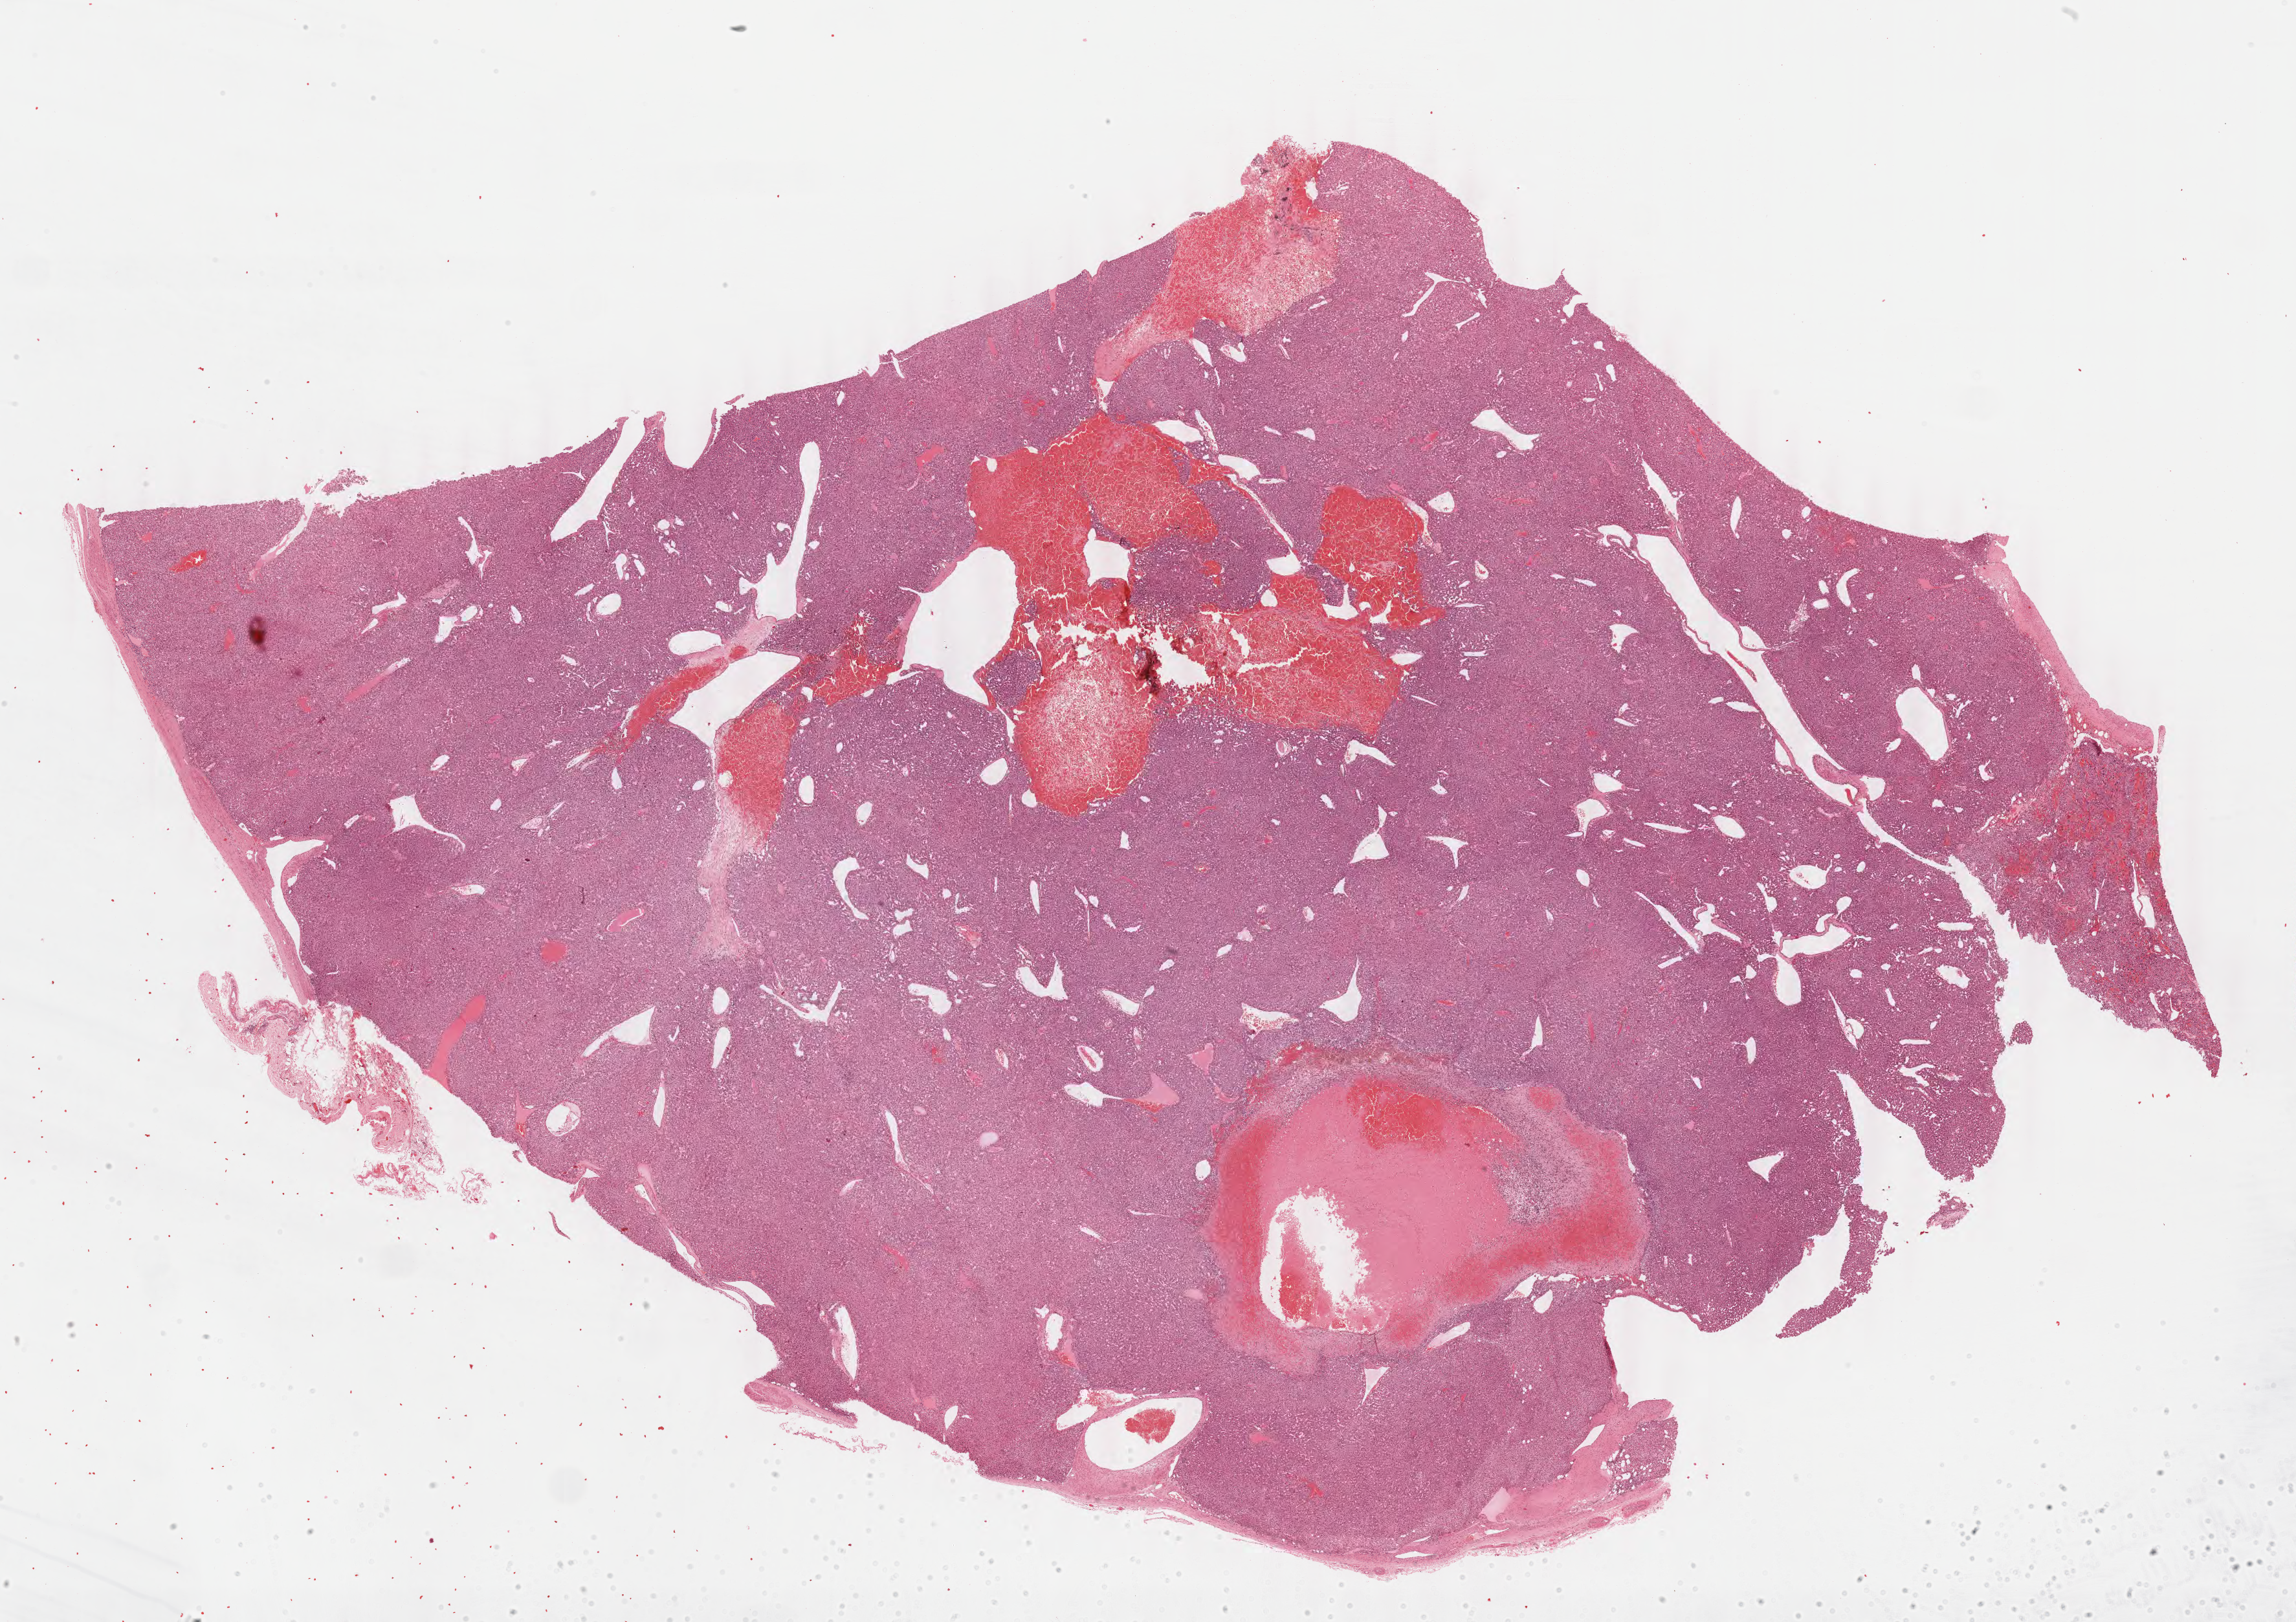
H&E whole-slide image — low-resolution overview of the scanned area, about 28.0 x 19.8 mm, formalin-fixed paraffin-embedded (FFPE) diagnostic section, primary tumour sample from the adrenal cortex. Female, age 27 years at initial diagnosis.
• pathologic diagnosis: Adrenal cortical carcinoma (cortex of adrenal gland)
• laterality: right